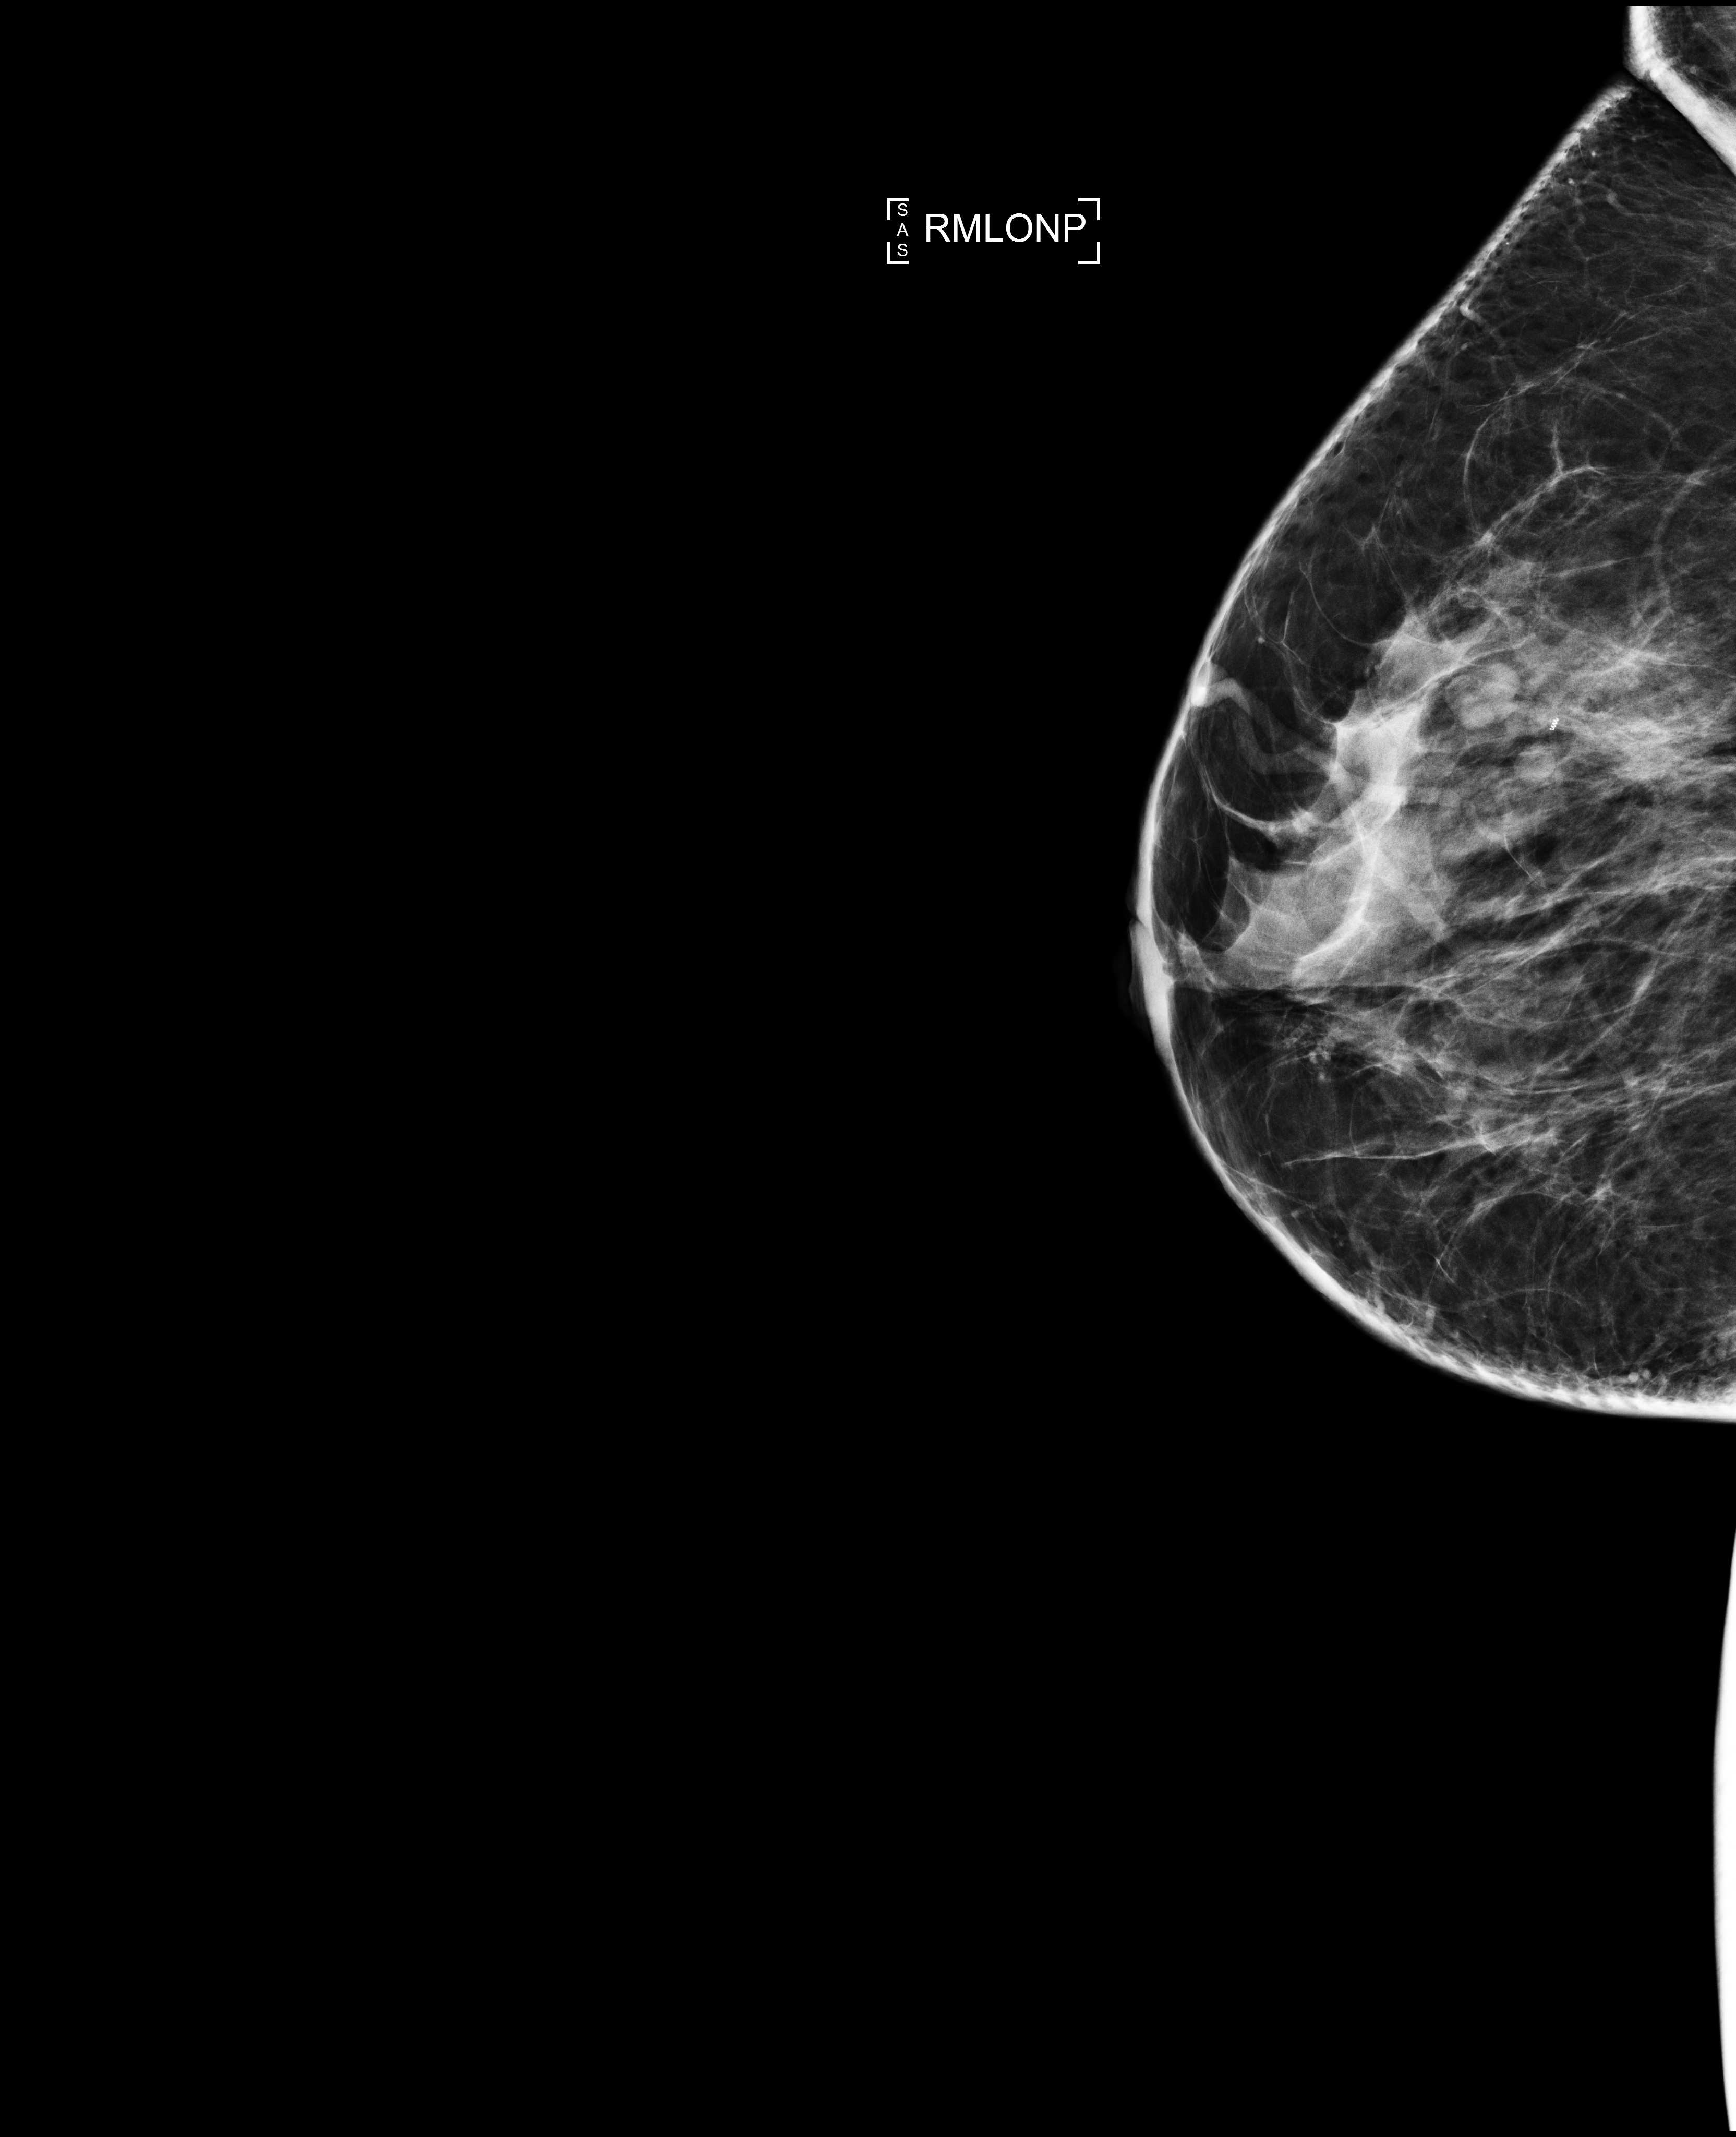
Full-field digital mammogram (FFDM); right breast; medio-lateral oblique projection (nipple in profile); annual screening mammography examination; compressed breast thickness 56 mm; system: Selenia Dimensions. Female patient, age 46 years.
Breast density at the screening exam (both breasts): heterogeneously dense (BI-RADS density category c). Final BI-RADS assessment for this screening round (tomosynthesis exam, both breasts): category 1. Recall: no recall after this screen.